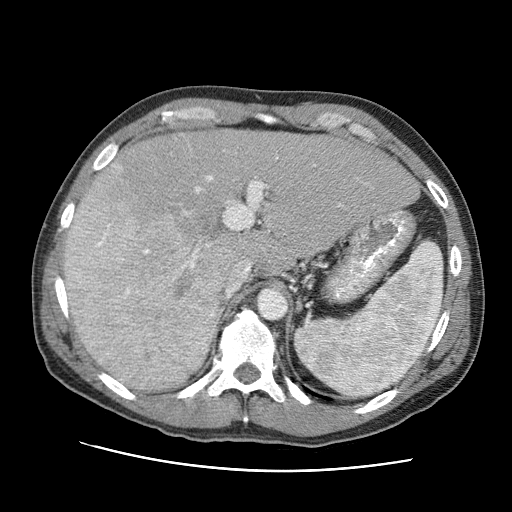
Contrast-enhanced abdominal CT (liver protocol), one axial slice; slice 63 of 95 in the series (ordered by position); 120 kVp; one of 2 acquisitions stored at this slice position; soft-tissue window (W 400 / L 40 HU); 2.5 mm slice thickness; 512 × 512 image matrix. From the clinical record (not read from this slice): diagnosis: hepatocellular carcinoma (patient treated with transarterial chemoembolisation; whether this scan precedes or follows treatment is not stated here); TNM stage (as recorded): Stage-IVA; Child-Pugh class: A; tumour differentiation: moderately differentiated; tumour nodularity: multinodular.
Structures marked on this image (semi-automatic segmentation, software-assisted and operator-edited):
- liver parenchyma outside the tumour (the mass and vessels are separate outlines, so this box may not span the whole liver): box from (x=64, y=130) to (x=418, y=390) px
- mass: (x=65, y=159)–(x=229, y=389)
- liver vessels: (x=179, y=164)–(x=368, y=363)